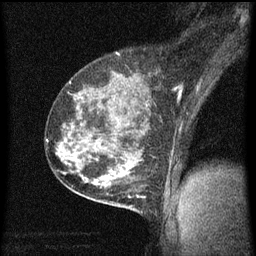
Breast MRI (dynamic contrast-enhanced), one sagittal slice. Position 42 of 60 along the scan axis. Dynamic contrast-enhanced series, image 2 of 3 at this slice position (ordered by acquisition). 1.5 T. TE 4.2 ms, TR 8 ms. 256 × 256 image matrix, field of view 180 × 180 mm. Female patient, age 35 years.
Outlined on this slice (semi-automatically segmented with operator editing):
- analysis volume of interest (the breast-tissue region the enhancement analysis was run in; not a lesion): bounding box <110,178,155,215> (left, top, right, bottom; pixels)
- tumour enhancement mask (voxels above the 70 % enhancement threshold inside the analysis volume of interest): <131,196,146,199>